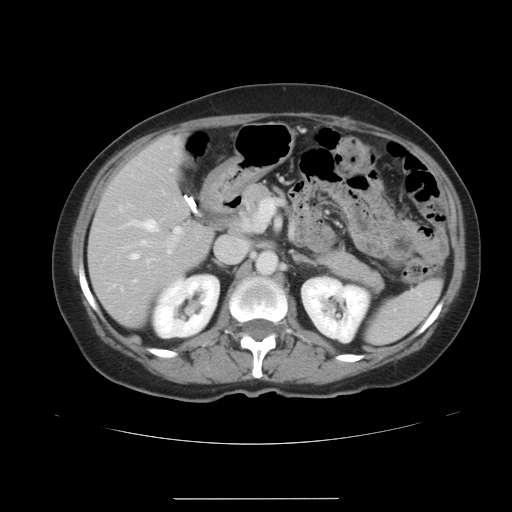
Contrast-enhanced abdominal CT, one axial slice. Slice 20 of 41 in the series (ordered by position). 120 kVp. Intravenous contrast given. Soft-tissue window (W 400 / L 40 HU). 512 × 512 image matrix, field of view 381 × 381 mm. Female patient, age 63 years. Case-level facts recorded for this patient, not image findings: diagnosis: colorectal cancer liver metastases, imaged before liver resection; multiple liver metastases: yes; largest metastasis: 1.5 cm; disease in both lobes: yes.
Annotated regions visible in this slice (outlined manually by an expert reader):
- hepatic veins: bounding box (x1, y1, x2, y2) in pixels: (129, 219, 157, 261)
- liver: (90, 135, 213, 325)
- planned liver remnant (the part of the liver to remain after resection): (90, 135, 213, 325)
- portal vein (with intrahepatic branches): (134, 227, 180, 282)